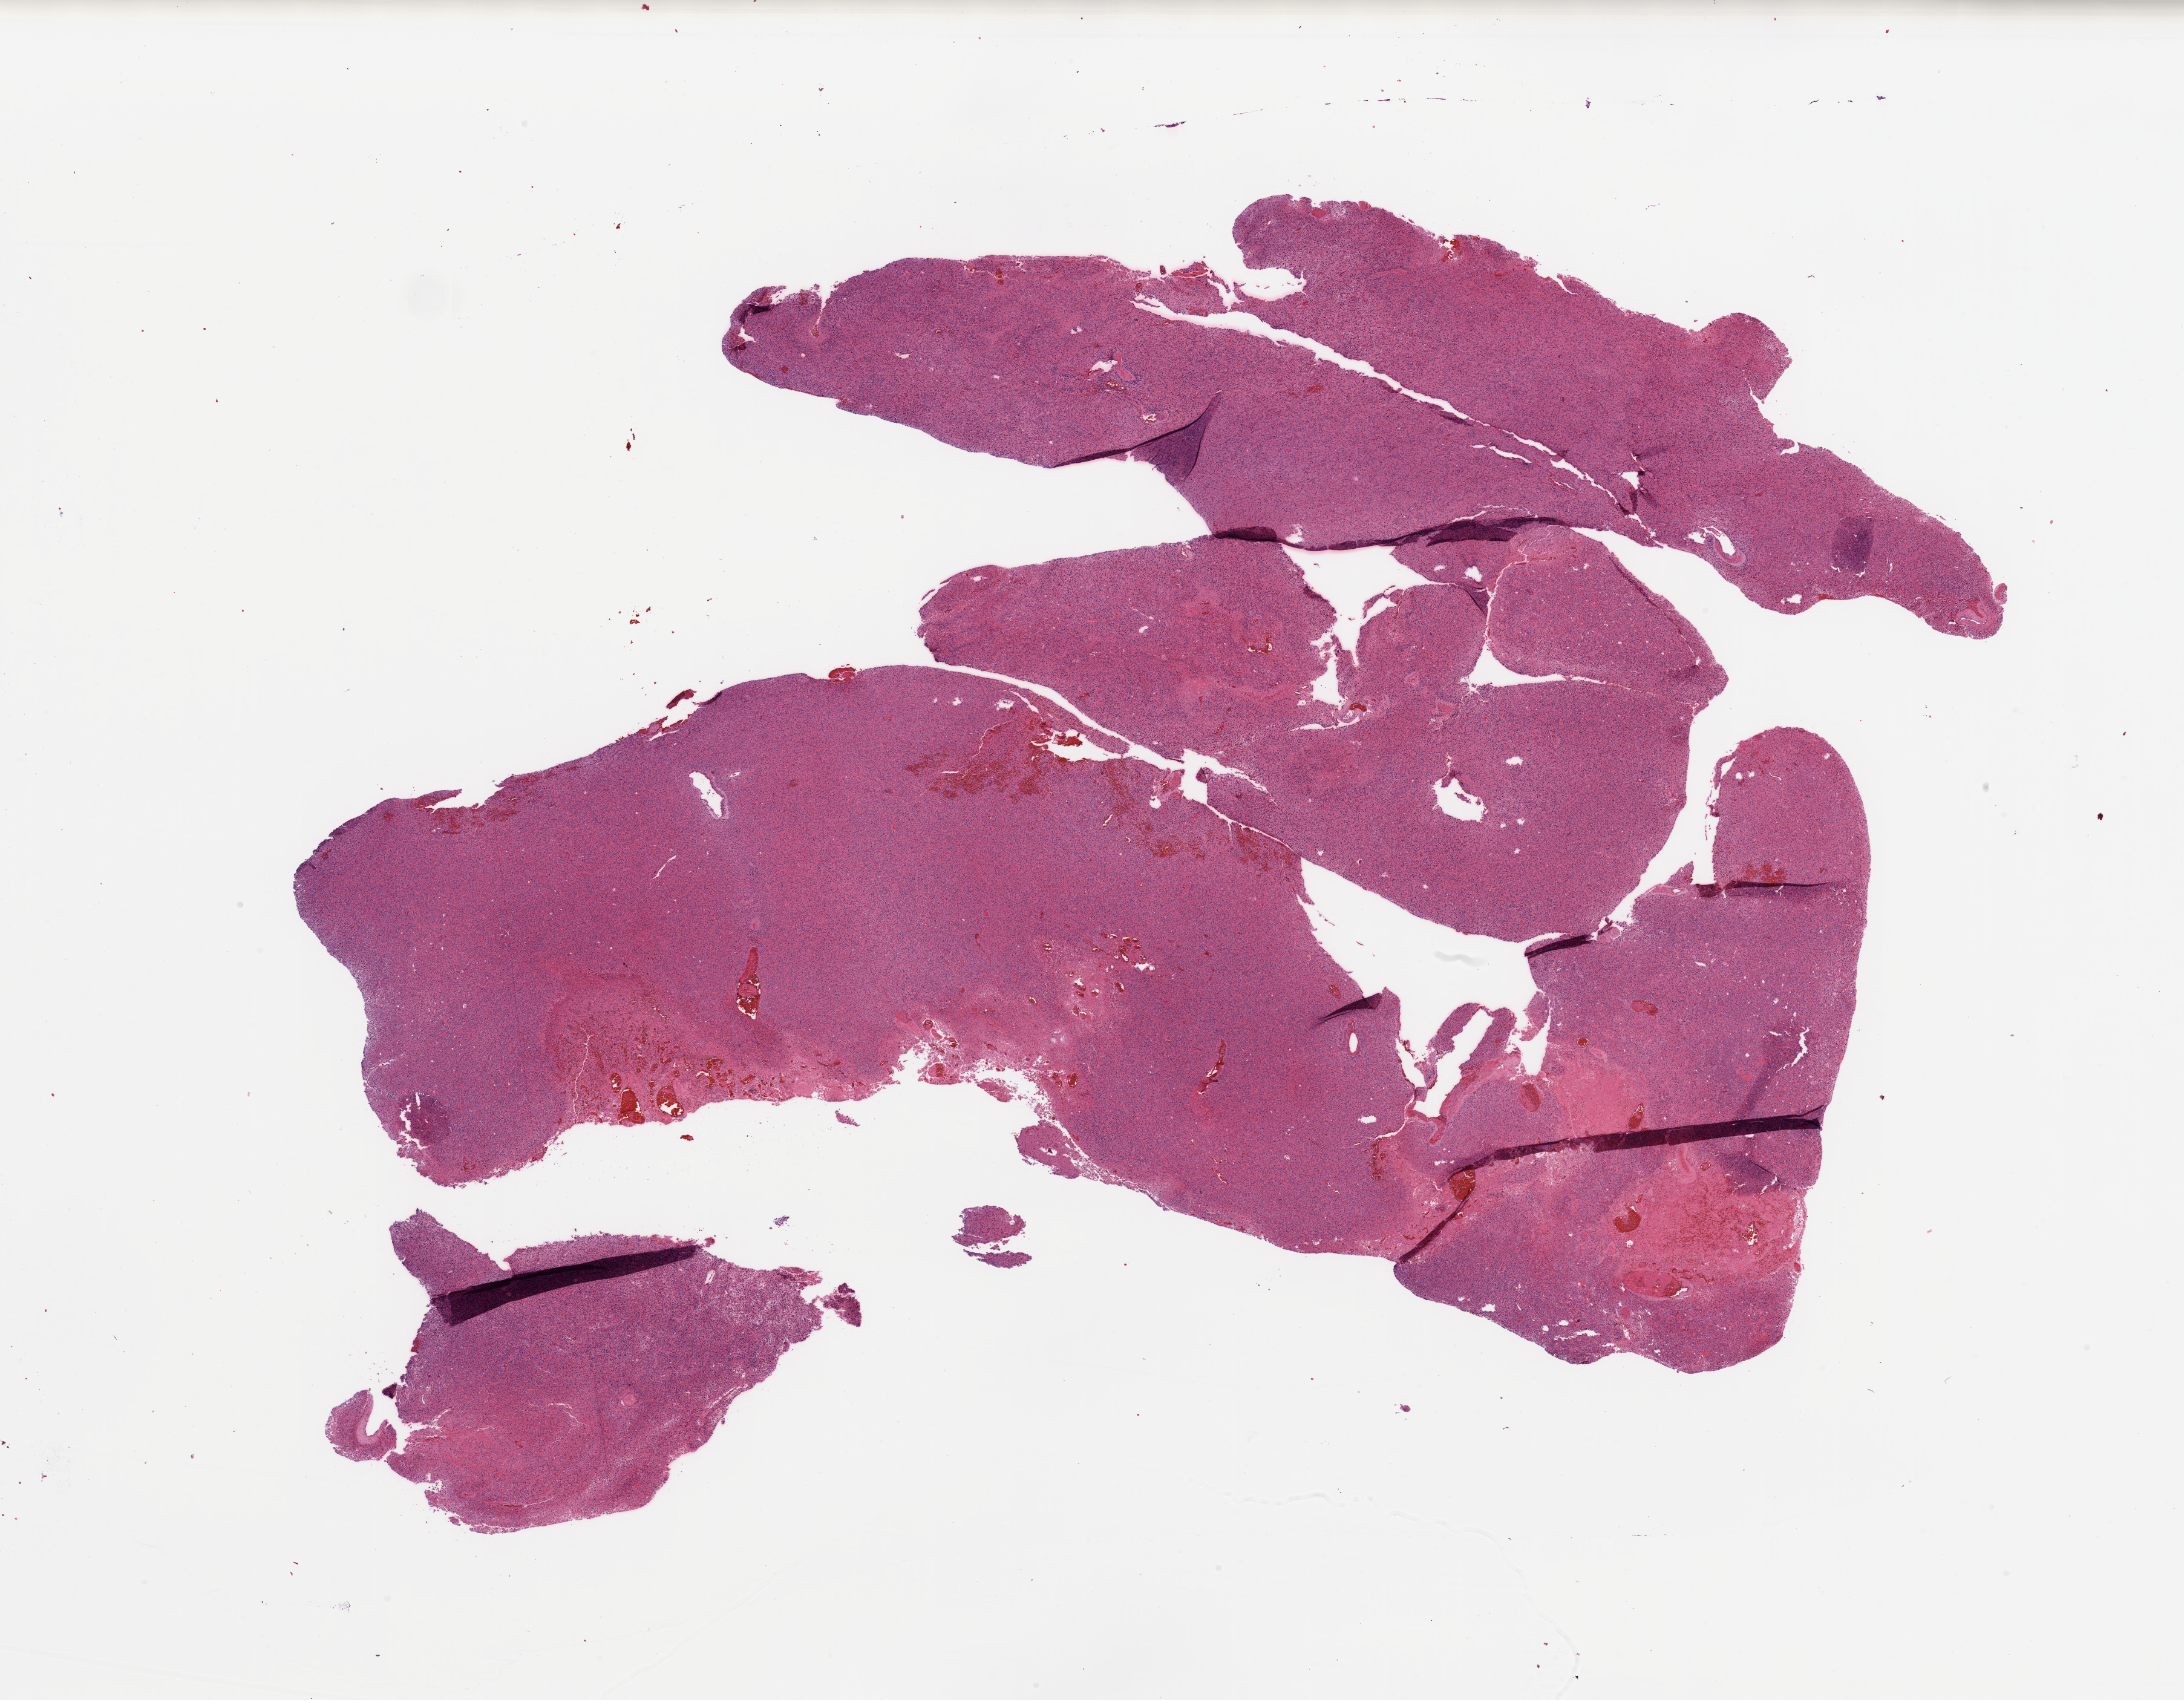
Digitized Hematoxylin and eosin (H&E) stained tissue section (whole slide), a low-resolution overview of the entire scanned area, about 28.5 x 22.2 mm (slide scanned at 20x). Tumour tissue sample, sampled site: brain. Female, 63 y/o. Slide review estimates, as recorded: tumour nuclei 90%, necrosis 5%.
Primary tumour site (as recorded): parietal lobe. Histologic diagnosis: Glioblastoma.